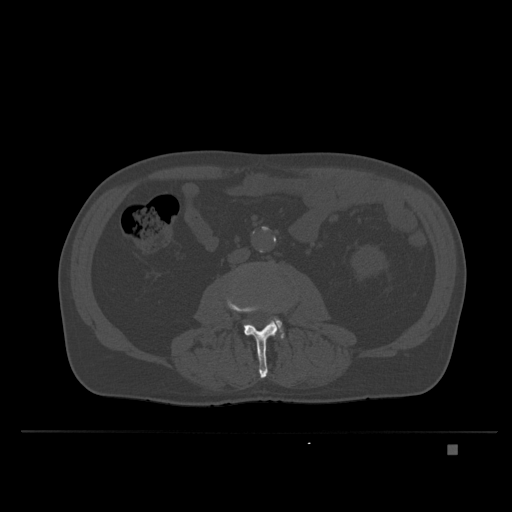
CT including the spine, one axial slice; slice 91 of 435 in the series (ordered by position); bone window (W 1800 / L 400 HU); 512 × 512 image matrix, field of view 434 × 434 mm. Patient: male, 73 years. From the clinical record (not read from this slice): primary cancer: skin.
Outlined on this slice (semi-automatic segmentation, software-assisted and operator-edited):
- L3 vertebra: bounding box <226,296,282,378> (left, top, right, bottom; pixels)
- L4 vertebra: <267,317,284,338>